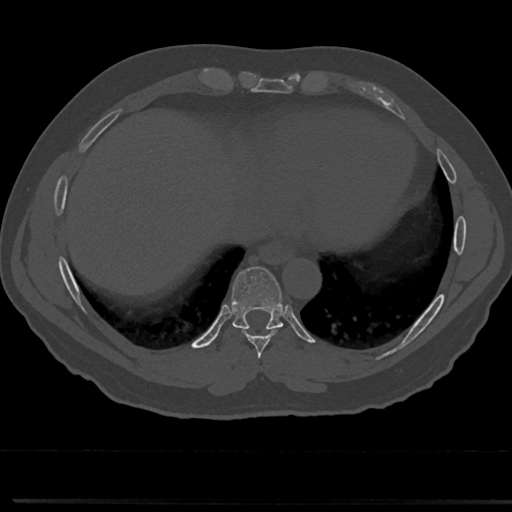
CT including the spine, one axial slice; position 328 of 817 along the scan axis; reconstruction kernel Br40s/3; 120 kVp; bone window (W 1800 / L 400 HU); 0.5 mm slice thickness; 512 × 512 image matrix, field of view 355 × 355 mm. Male patient, age 61 years. From the clinical record (not read from this slice): primary cancer: prostate.
Structures marked on this image (semi-automatically segmented with operator editing):
- T7 vertebra: bounding box [x1, y1, x2, y2] px = [258, 351, 266, 376]
- T8 vertebra: [211, 270, 310, 357]